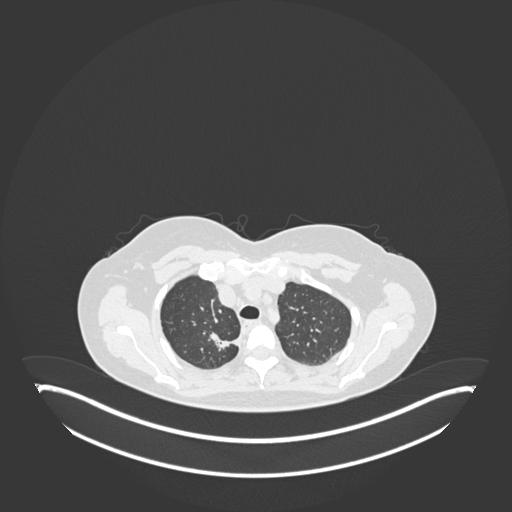
Chest CT, one axial slice; slice 143 of 181 in the series (ordered by position); 120 kVp; lung window (W 1500 / L -600 HU); 1 mm slice thickness; 512 × 512 image matrix, field of view 500 × 500 mm. Female patient, age 65 years. Case-level facts recorded for this patient, not image findings: clinical TNM (as recorded): T1b N0 M0; histopathological grade: G2.
Outlined on this slice (bounding box drawn by a radiologist):
- lung tumour (recorded histology: adenocarcinoma): box from (x=206, y=328) to (x=245, y=354) px